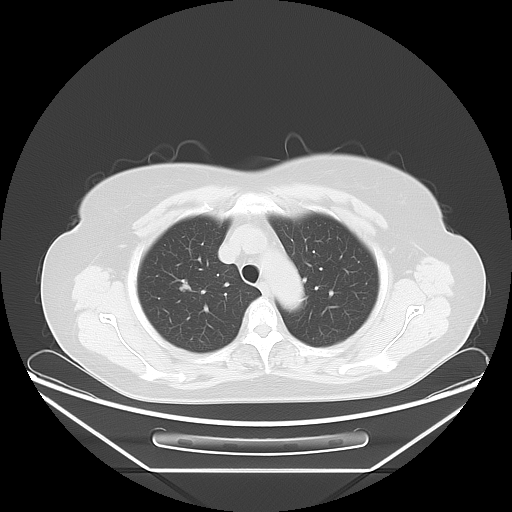
Chest CT, one axial slice; slice 48 of 59 in the series (ordered by position); lung window (W 1500 / L -600 HU); 5 mm slice thickness; 512 × 512 image matrix, field of view 433 × 433 mm. Patient: female, 60 years. Case-level facts recorded for this patient, not image findings: clinical TNM (as recorded): T1c N0 M0.
Outlined on this slice (bounding box drawn by a radiologist):
- lung tumour (recorded histology: adenocarcinoma): bounding box (x1, y1, x2, y2) in pixels: (175, 271, 197, 296)